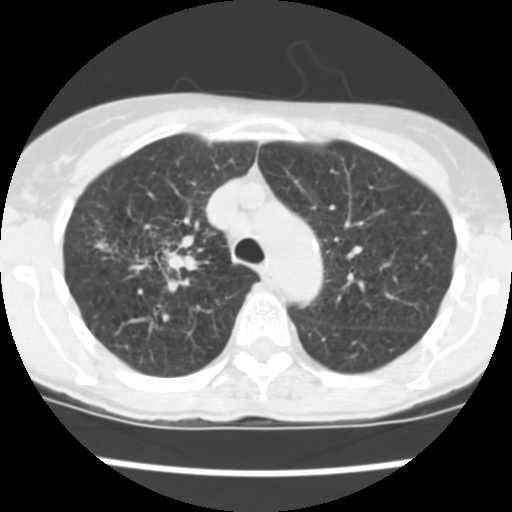
Low-dose screening chest CT, one axial slice. Slice 181 of 252 in the series (ordered by position). Reconstruction kernel STANDARD. 120 kVp. Lung window (W 1500 / L -600 HU). 2.5 mm slice thickness. 512 × 512 image matrix, field of view 276 × 276 mm.
Annotated regions visible in this slice (expert manual segmentation):
- lesion 2 (tumor, lower lobe of right lung): bounding box [x1, y1, x2, y2] px = [165, 251, 194, 270]